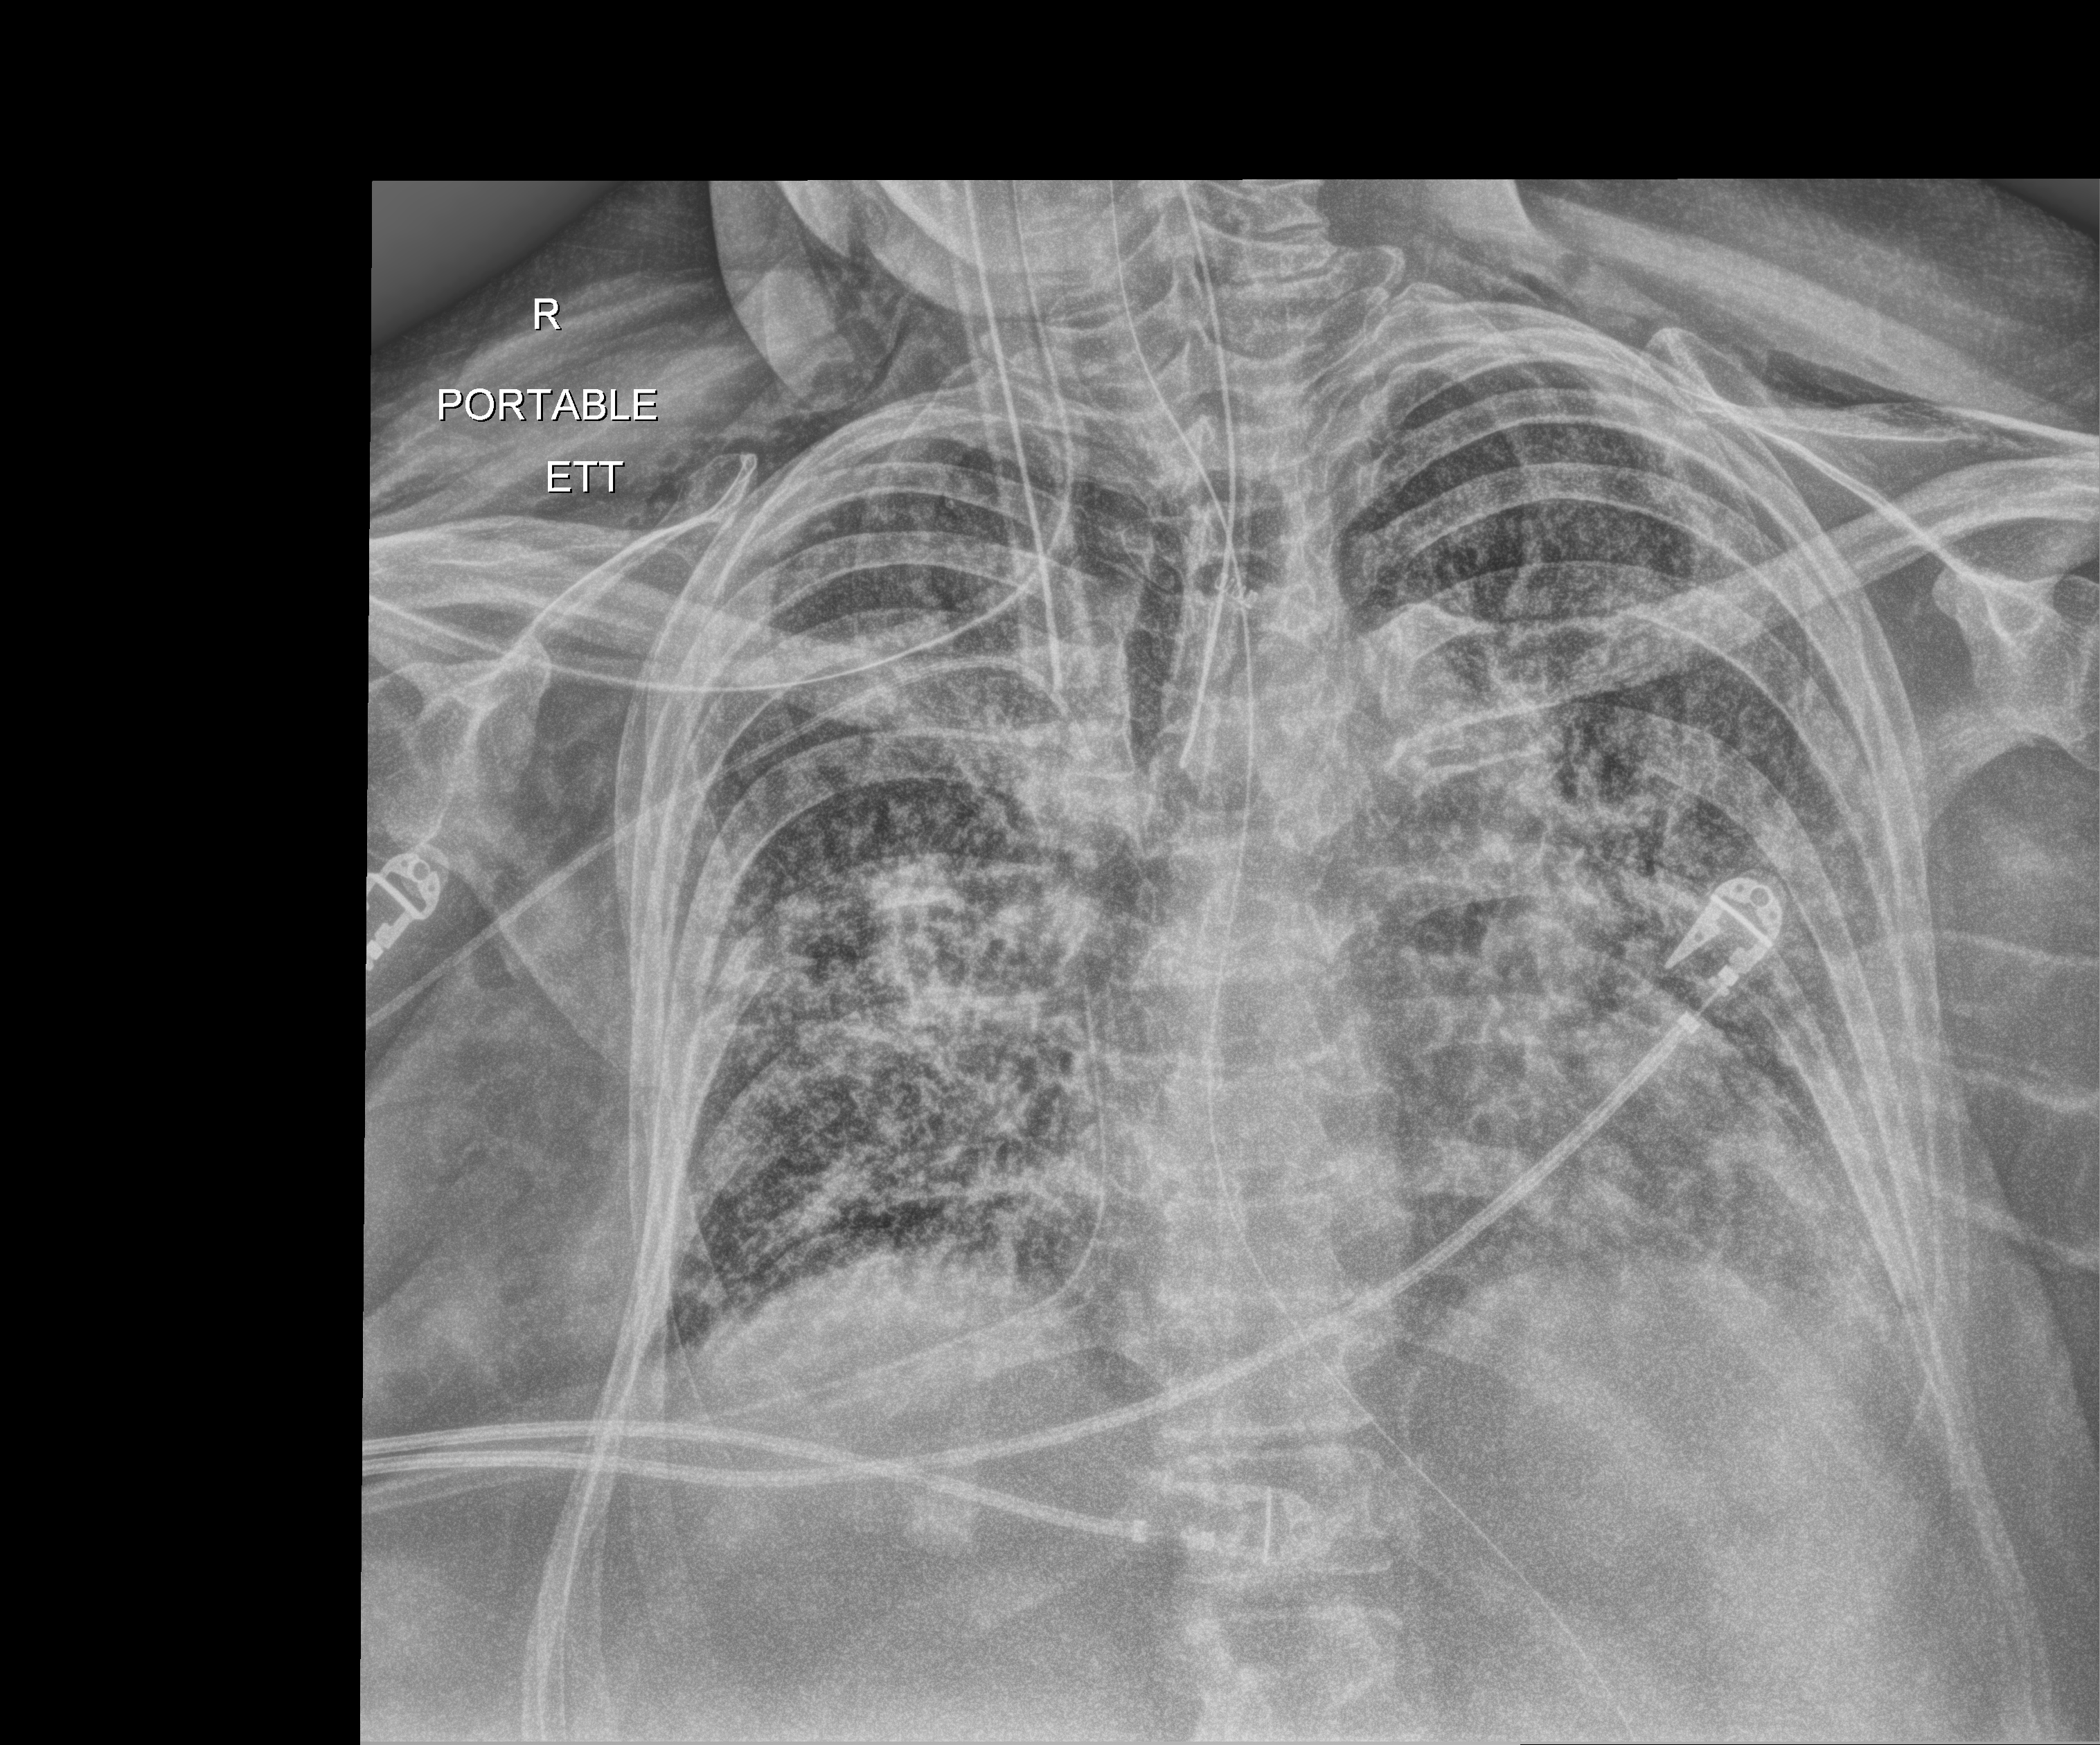
Chest radiograph; anteroposterior (AP) projection. Female patient hospitalised with COVID-19, age 60–74 years.
Admission-level facts for this patient (not findings on this image; timing relative to this image not recorded): COPD (admission record): no.